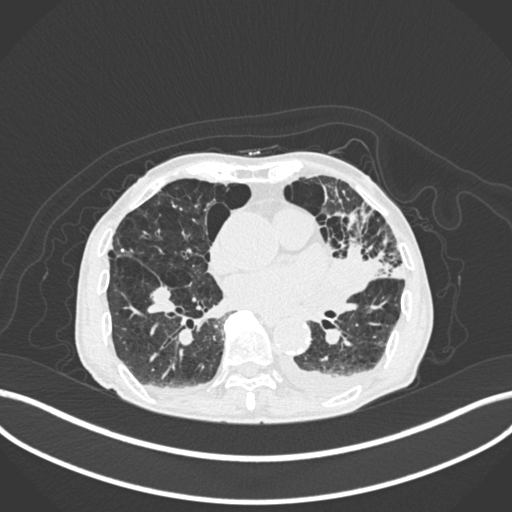
Chest CT, one axial slice. Slice 91 of 400 in the series (ordered by position). 120 kVp. Lung window (W 1500 / L -600 HU). 1 mm slice thickness. 512 × 512 image matrix, field of view 400 × 400 mm. Male patient, age 90 years or older. From the clinical record (not read from this slice): clinical TNM (as recorded): T2b N1 M0.
Annotated regions visible in this slice (rectangle marked by the reading radiologist):
- lung tumour (recorded histology: squamous cell carcinoma): bounding box <333,238,383,298> (left, top, right, bottom; pixels)